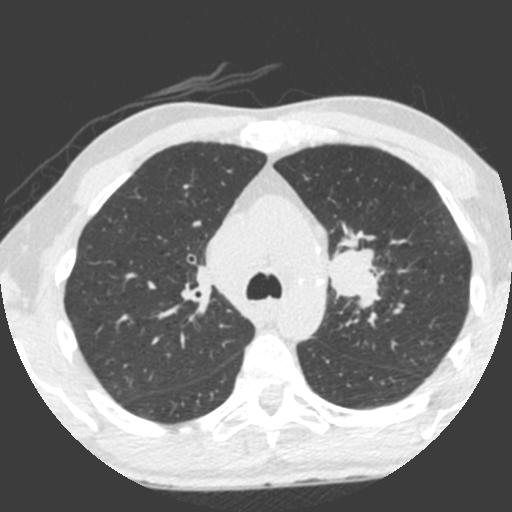
Low-dose screening chest CT, one axial slice. Lung window (W 1500 / L -600 HU). 512 × 512 image matrix, field of view 315 × 315 mm.
Outlined on this slice (expert manual segmentation):
- lesion 1 (tumor, upper lobe of left lung): bounding box (x1, y1, x2, y2) in pixels: (328, 246, 381, 309)